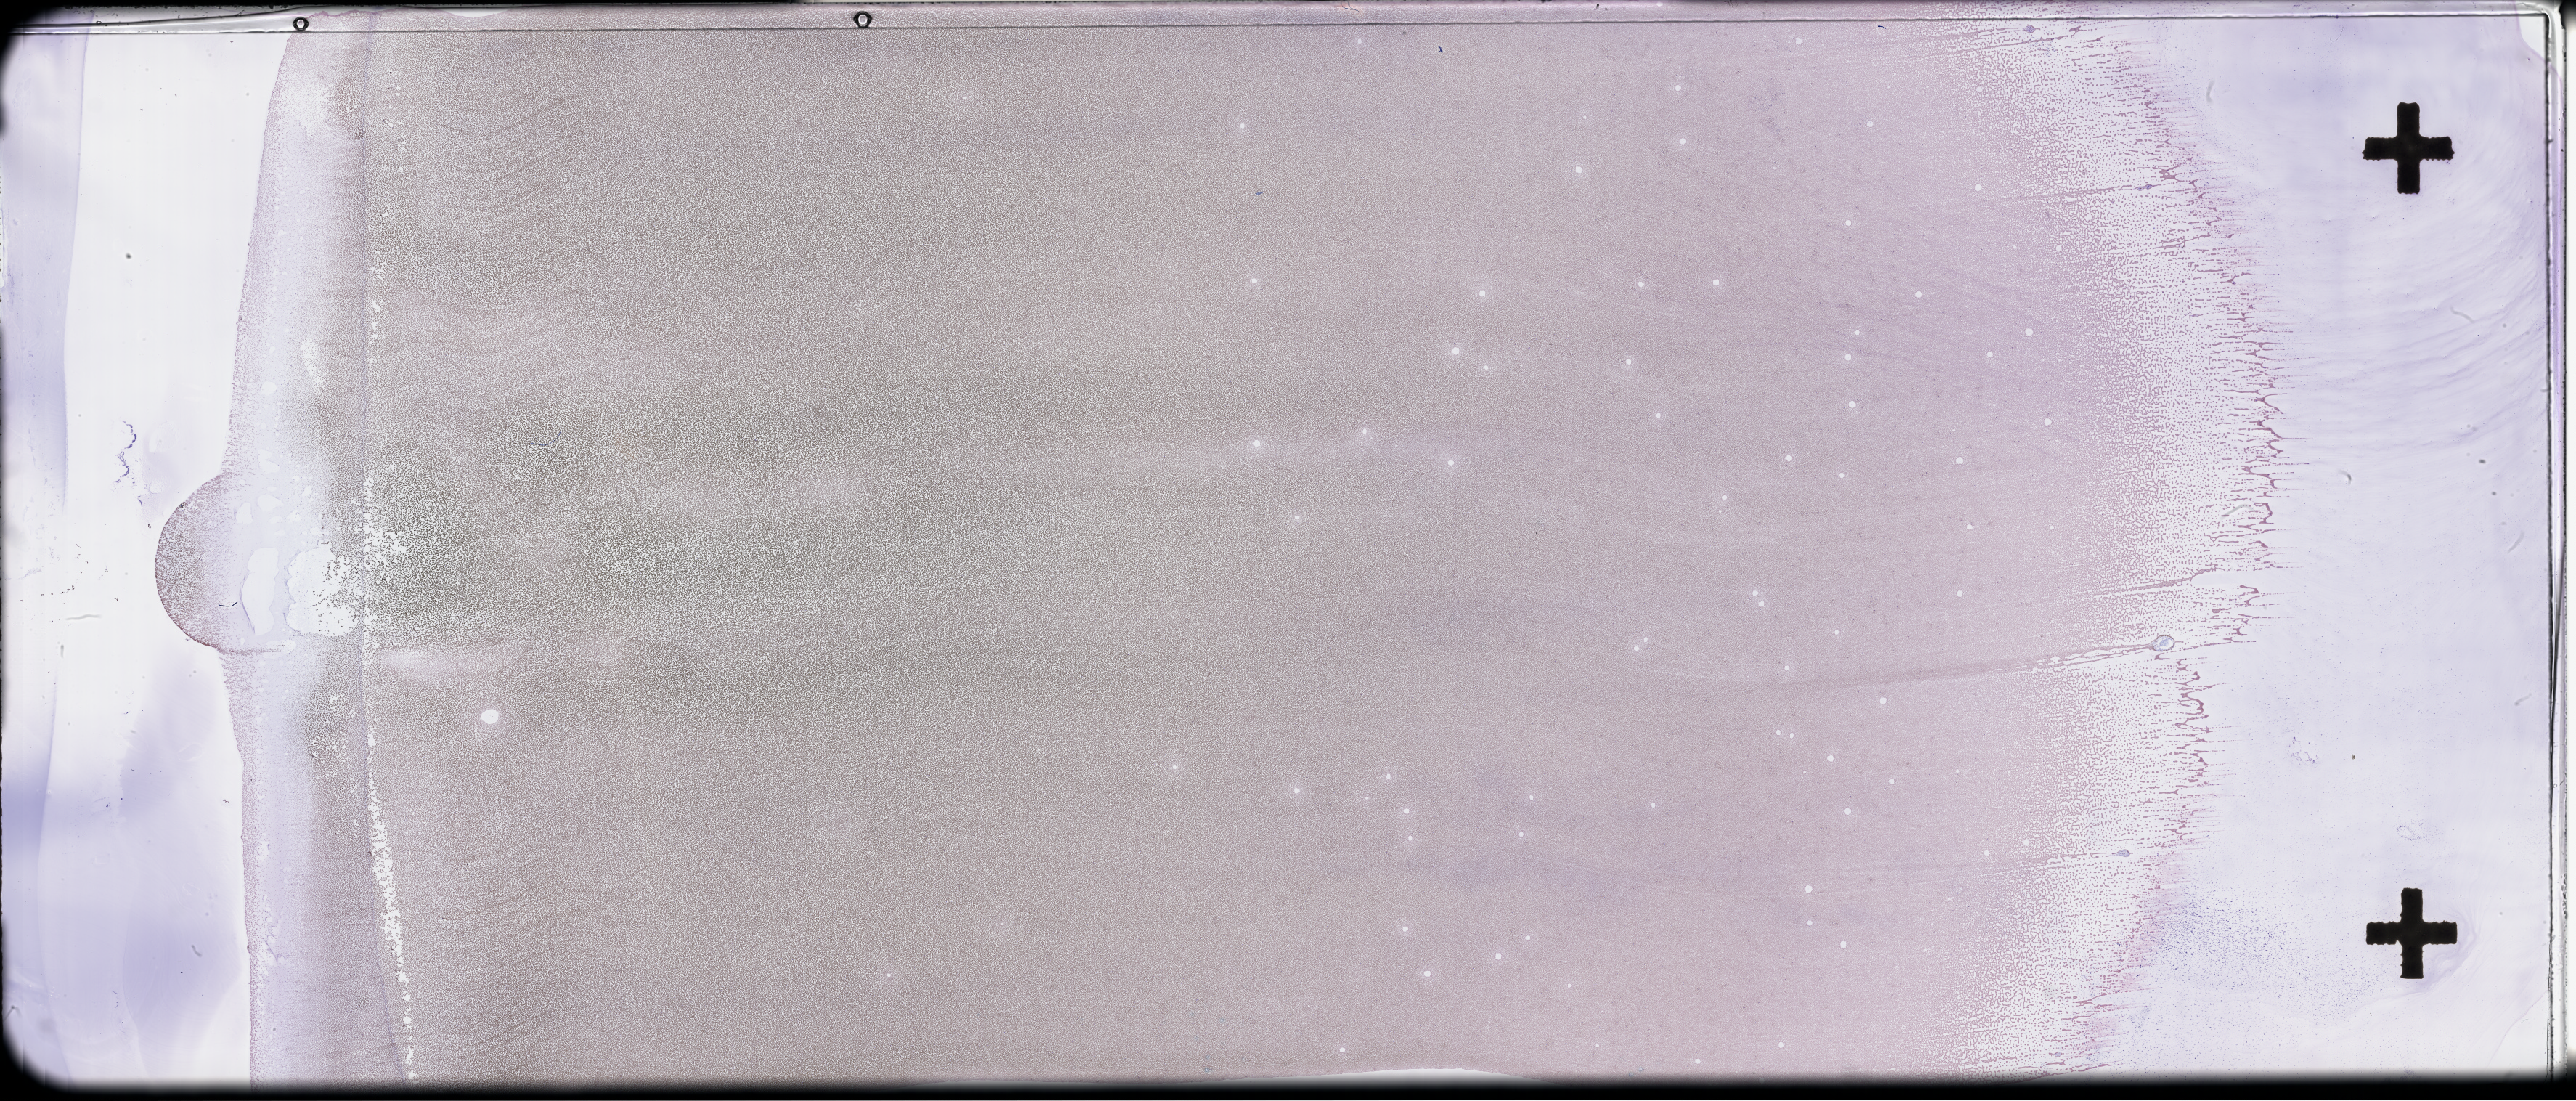
Whole-slide image of a whole blood smear, Wright–Giemsa stain — whole scanned area (about 57.3 x 24.5 mm) shown as a low-resolution overview, smear from an EDTA sample, collected on treatment. Male patient.
From a patient with: Plasma Cell Myeloma.